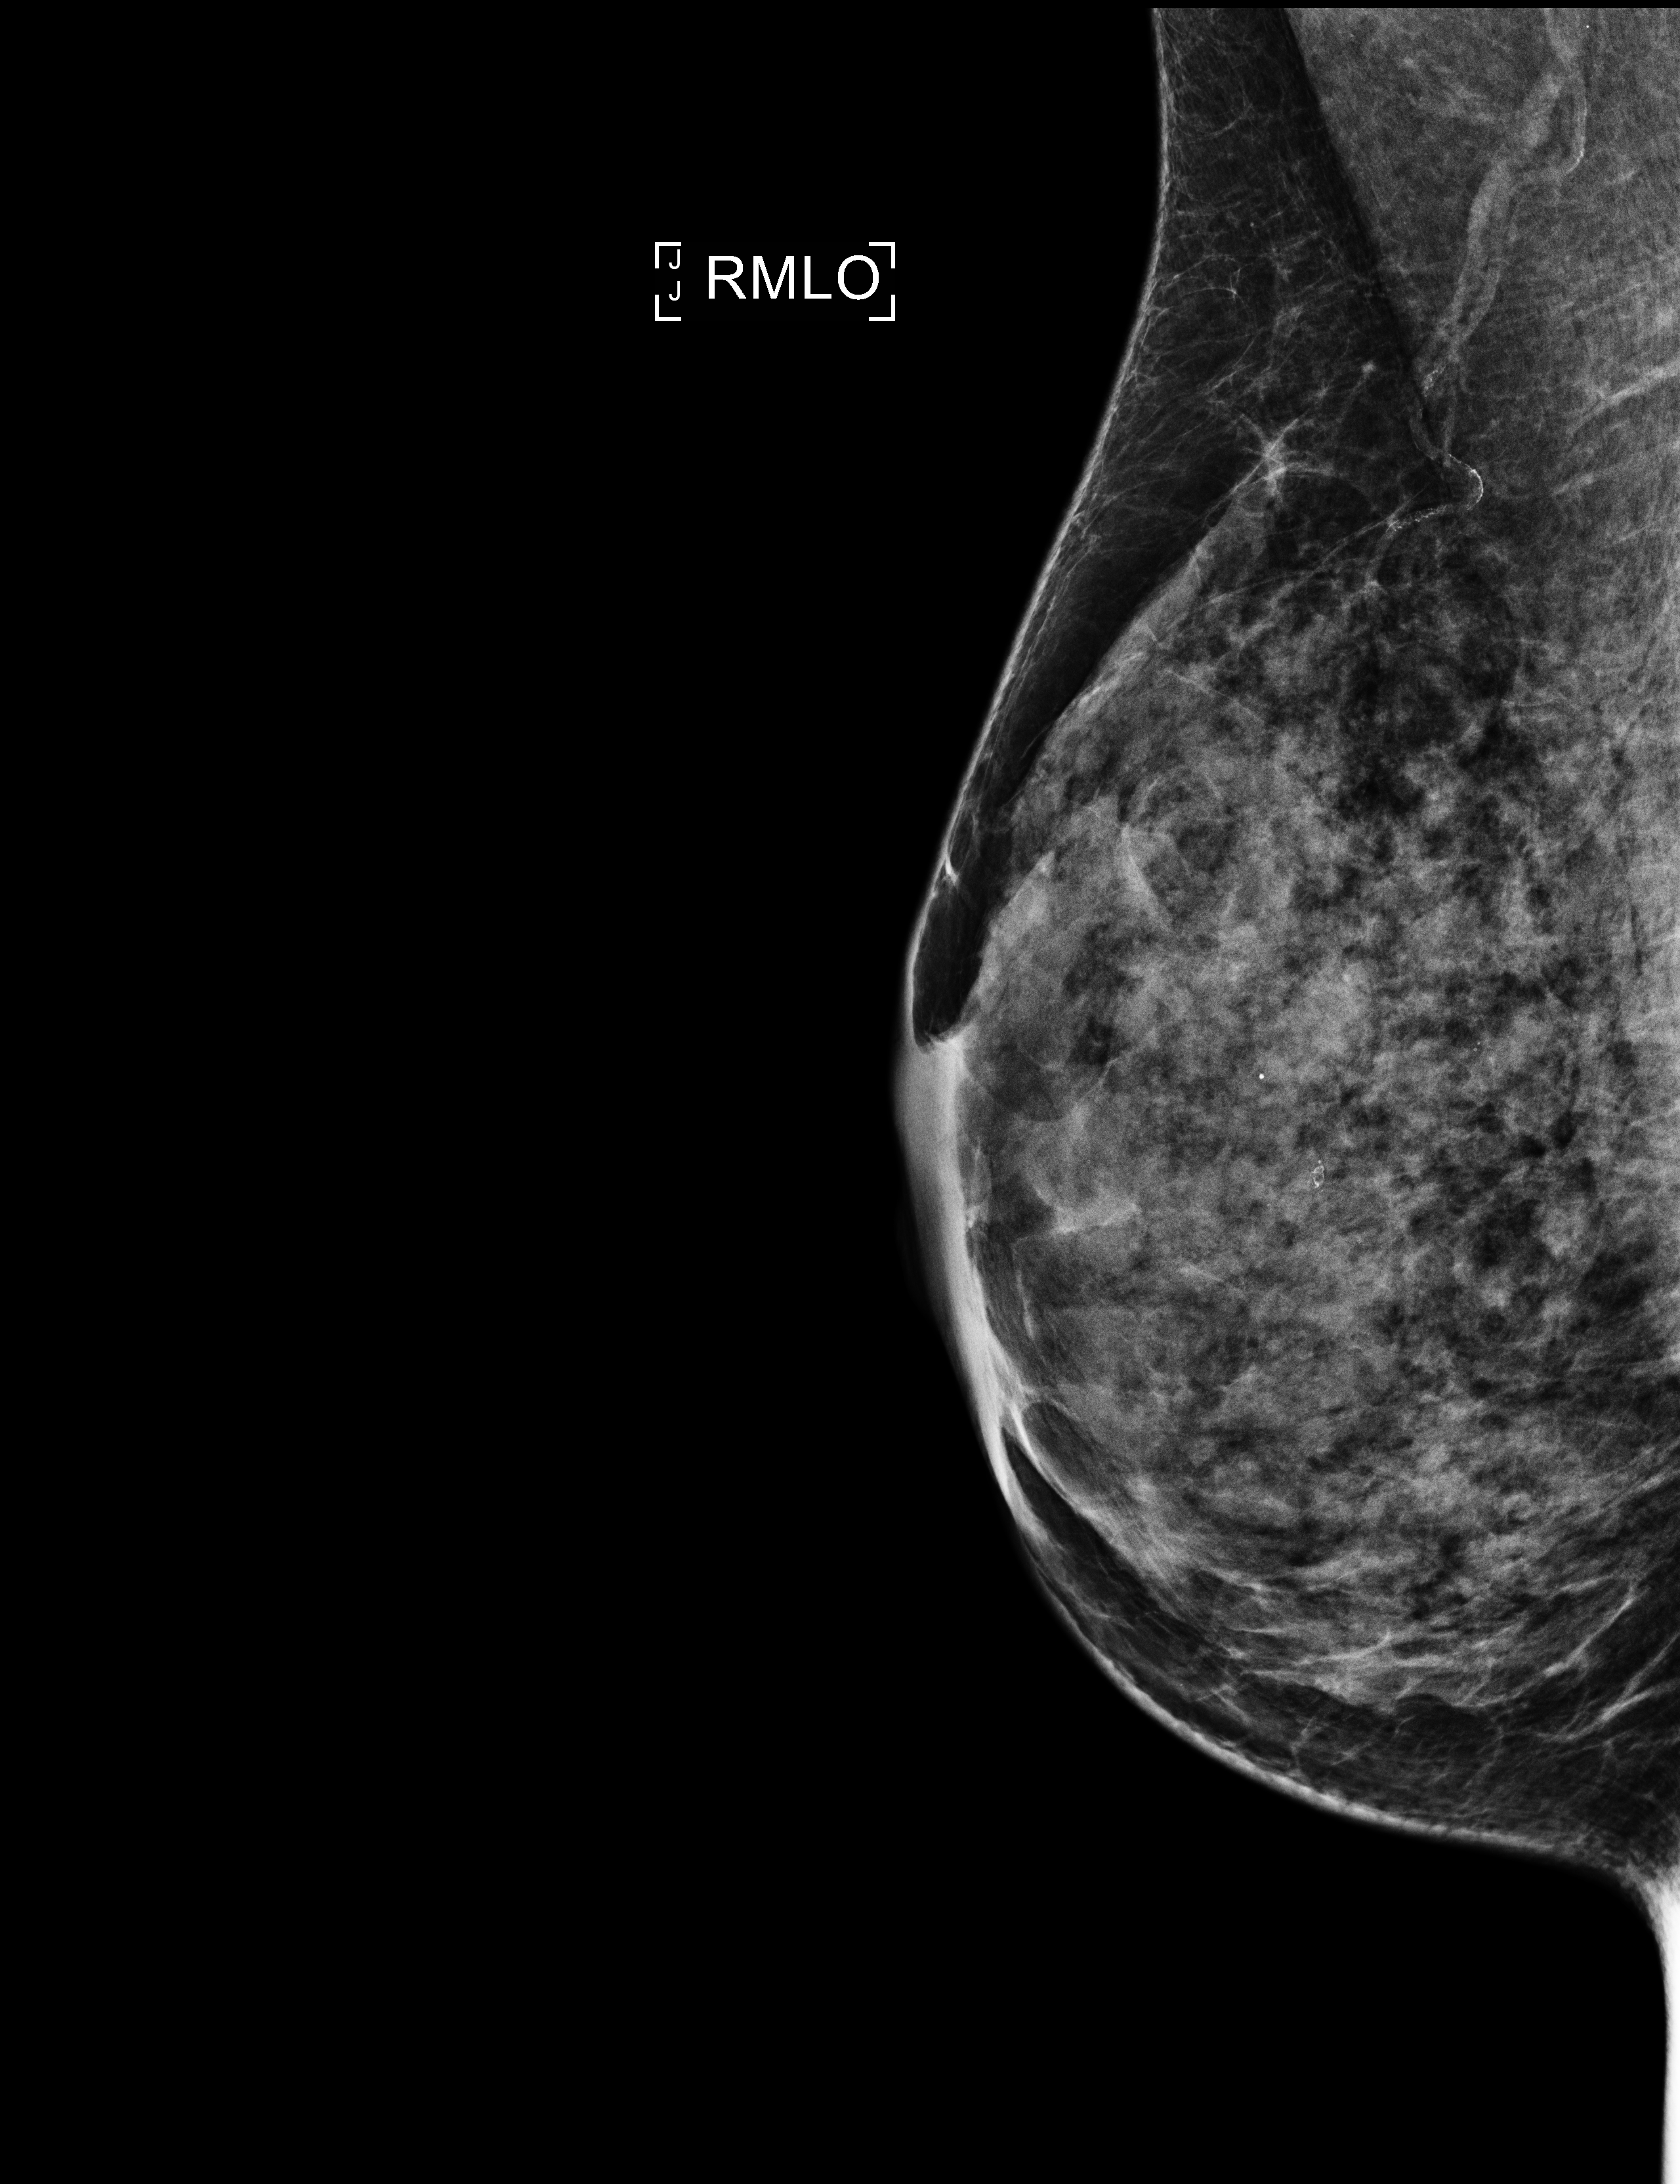
Full-field digital mammogram (FFDM), right breast, medio-lateral oblique projection, screening examination, compressed breast thickness 41 mm. Patient aged 56 years (female).
BI-RADS breast density category at the screening exam (both breasts, scale 1–4): 1. Final BI-RADS assessment for this screening round (tomosynthesis exam, both breasts): category 1. Recall: no recall after this screen.